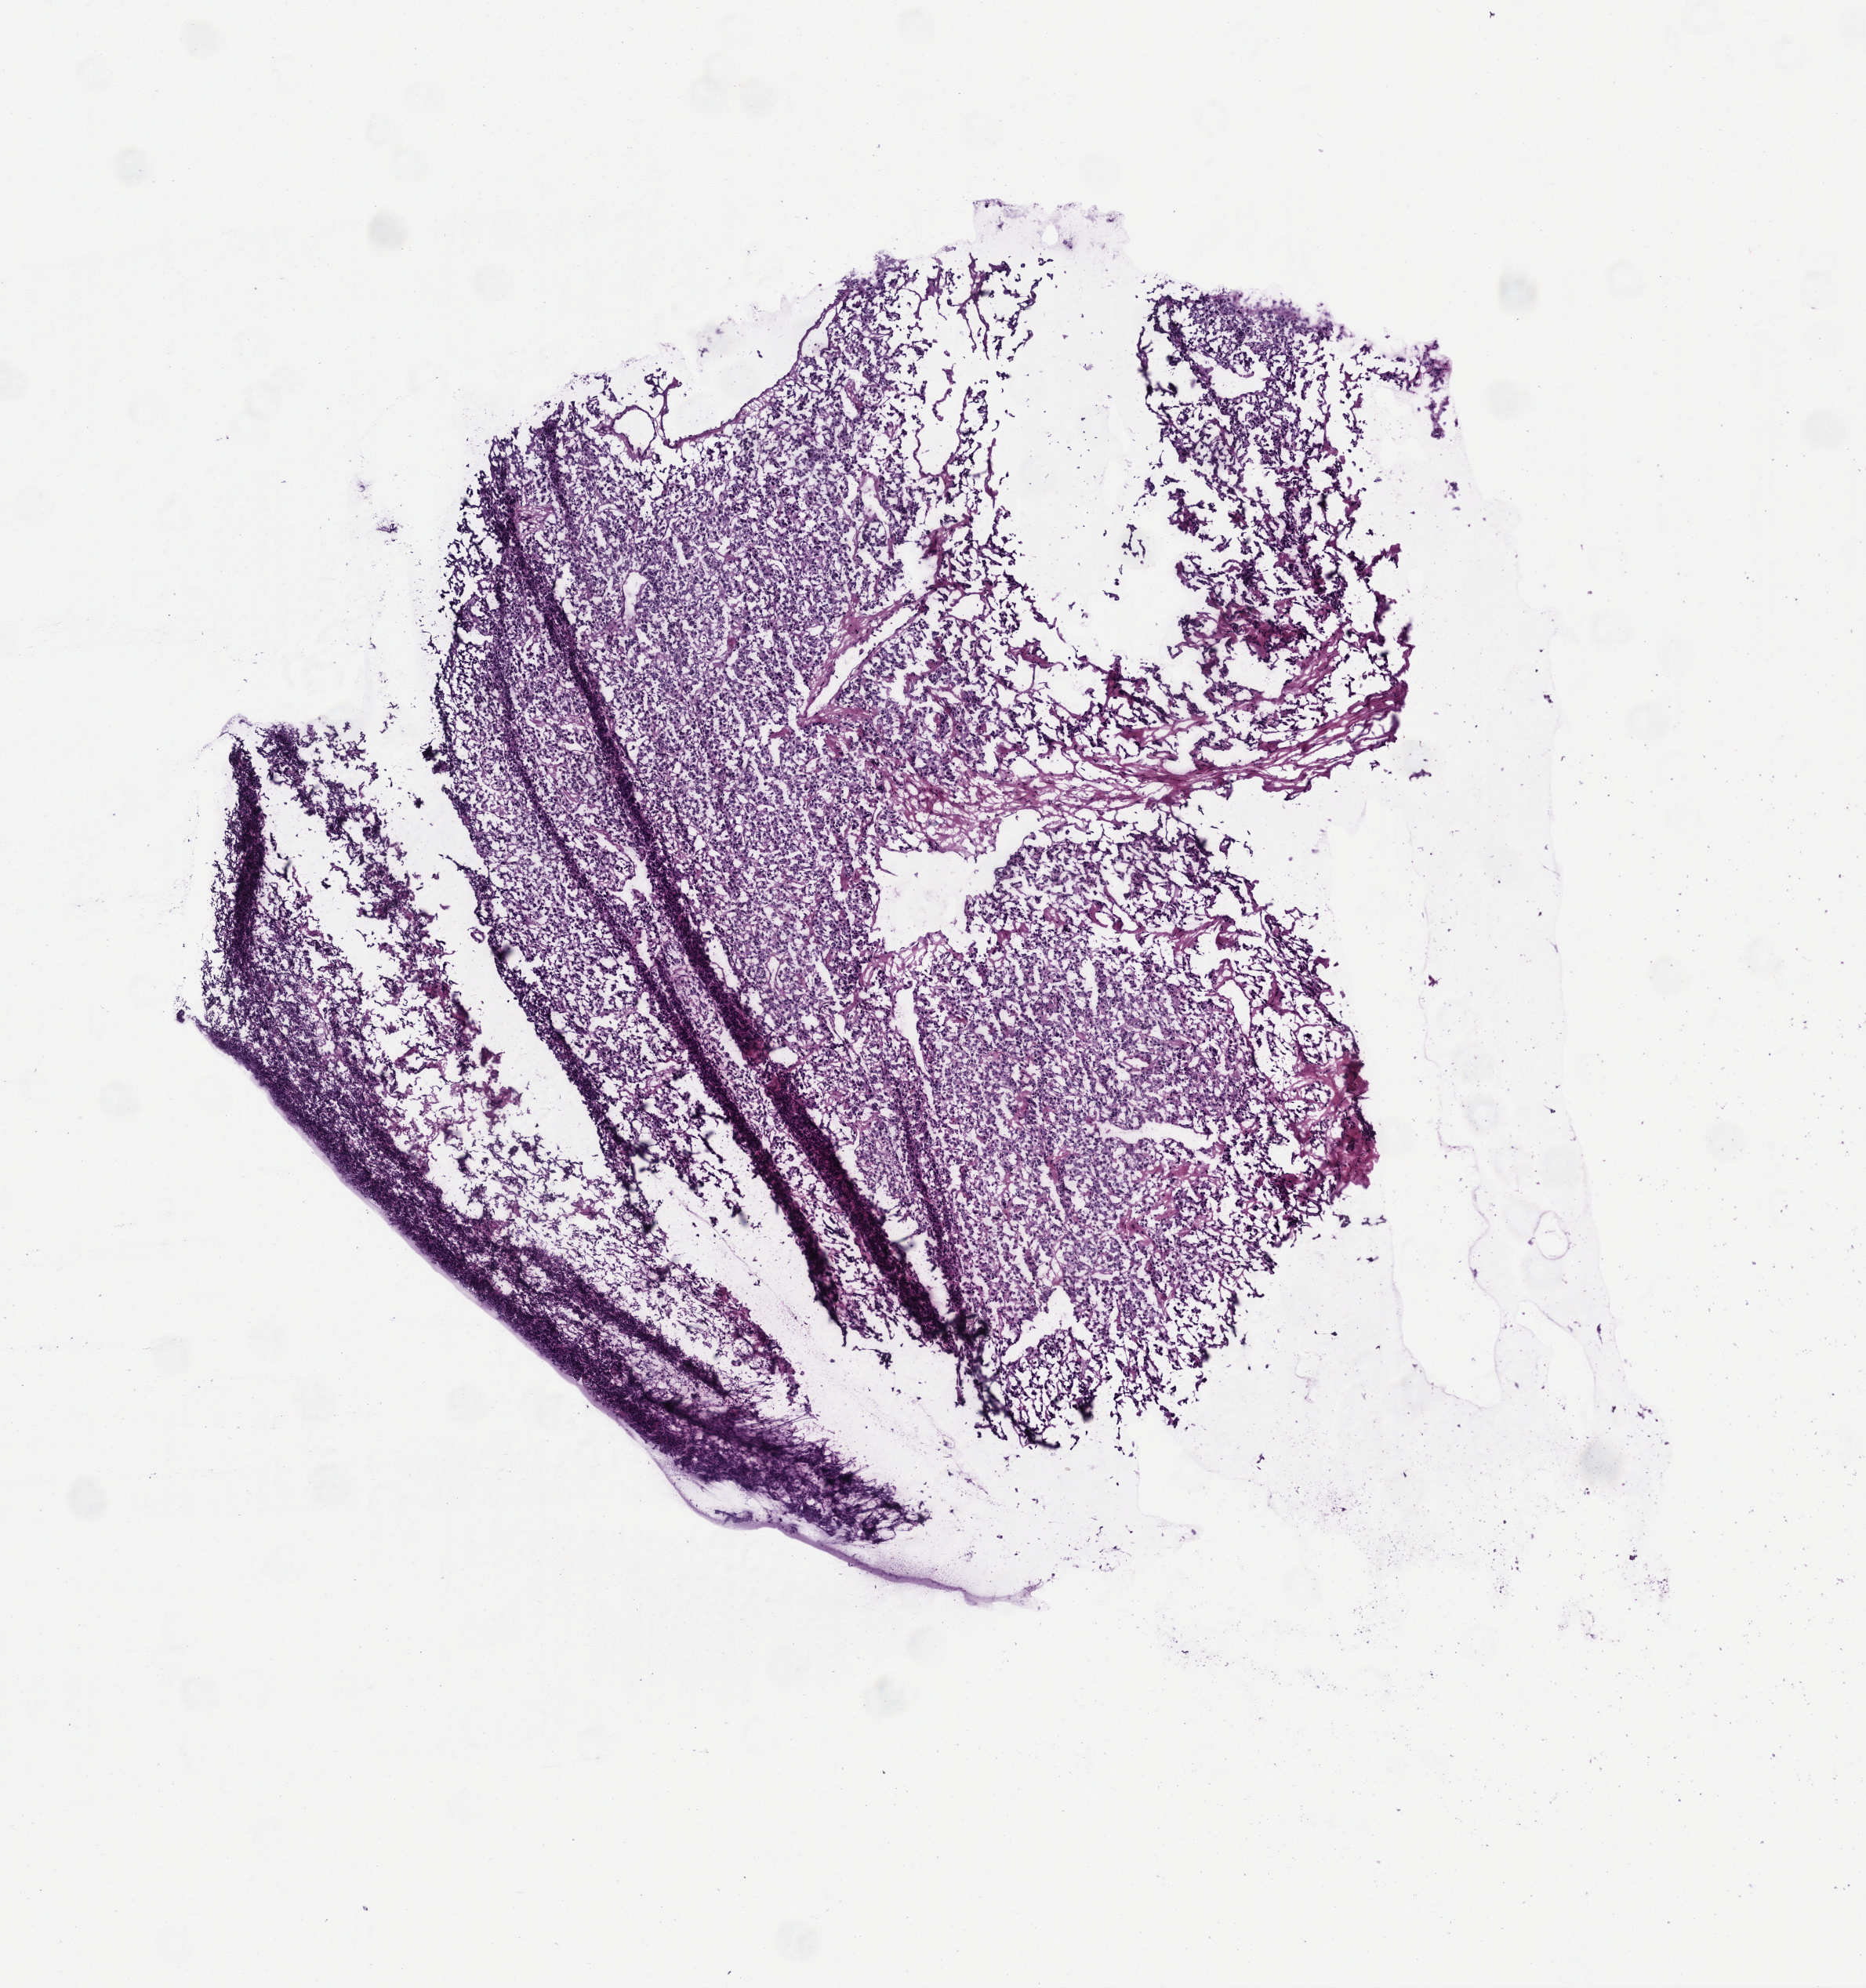
Digitized H&E tissue section (whole slide) — a low-resolution overview of the entire scanned area, about 4.7 x 5.0 mm (from a 40x scan), frozen section from the top of the tissue portion, adrenal gland, primary tumour sample. Patient: female, age at initial diagnosis 45 years. Slide review estimates, as recorded: tumour cells 100%, tumour nuclei 95%, normal cells 0%, stromal cells 0%, necrosis 0%. Infiltration values recorded for this section: lymphocyte infiltration 0%, monocyte infiltration 0%, neutrophil infiltration 0%.
• laterality: left
• diagnosis: Pheochromocytoma, NOS